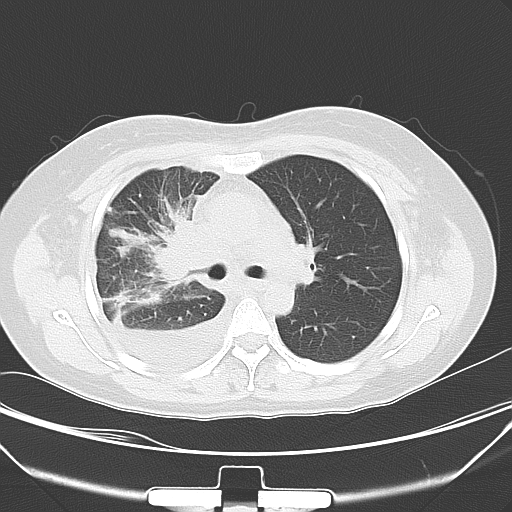
Chest CT, one axial slice. Slice 34 of 52 in the series (ordered by position). Lung window (W 1500 / L -600 HU). 5 mm slice thickness. 512 × 512 image matrix. Patient: female, 36 years. From the clinical record (not read from this slice): clinical TNM (as recorded): T1b N2 M0.
Structures marked on this image (bounding box drawn by a radiologist):
- lung tumour (recorded histology: adenocarcinoma): bounding box <142,207,206,286> (left, top, right, bottom; pixels)